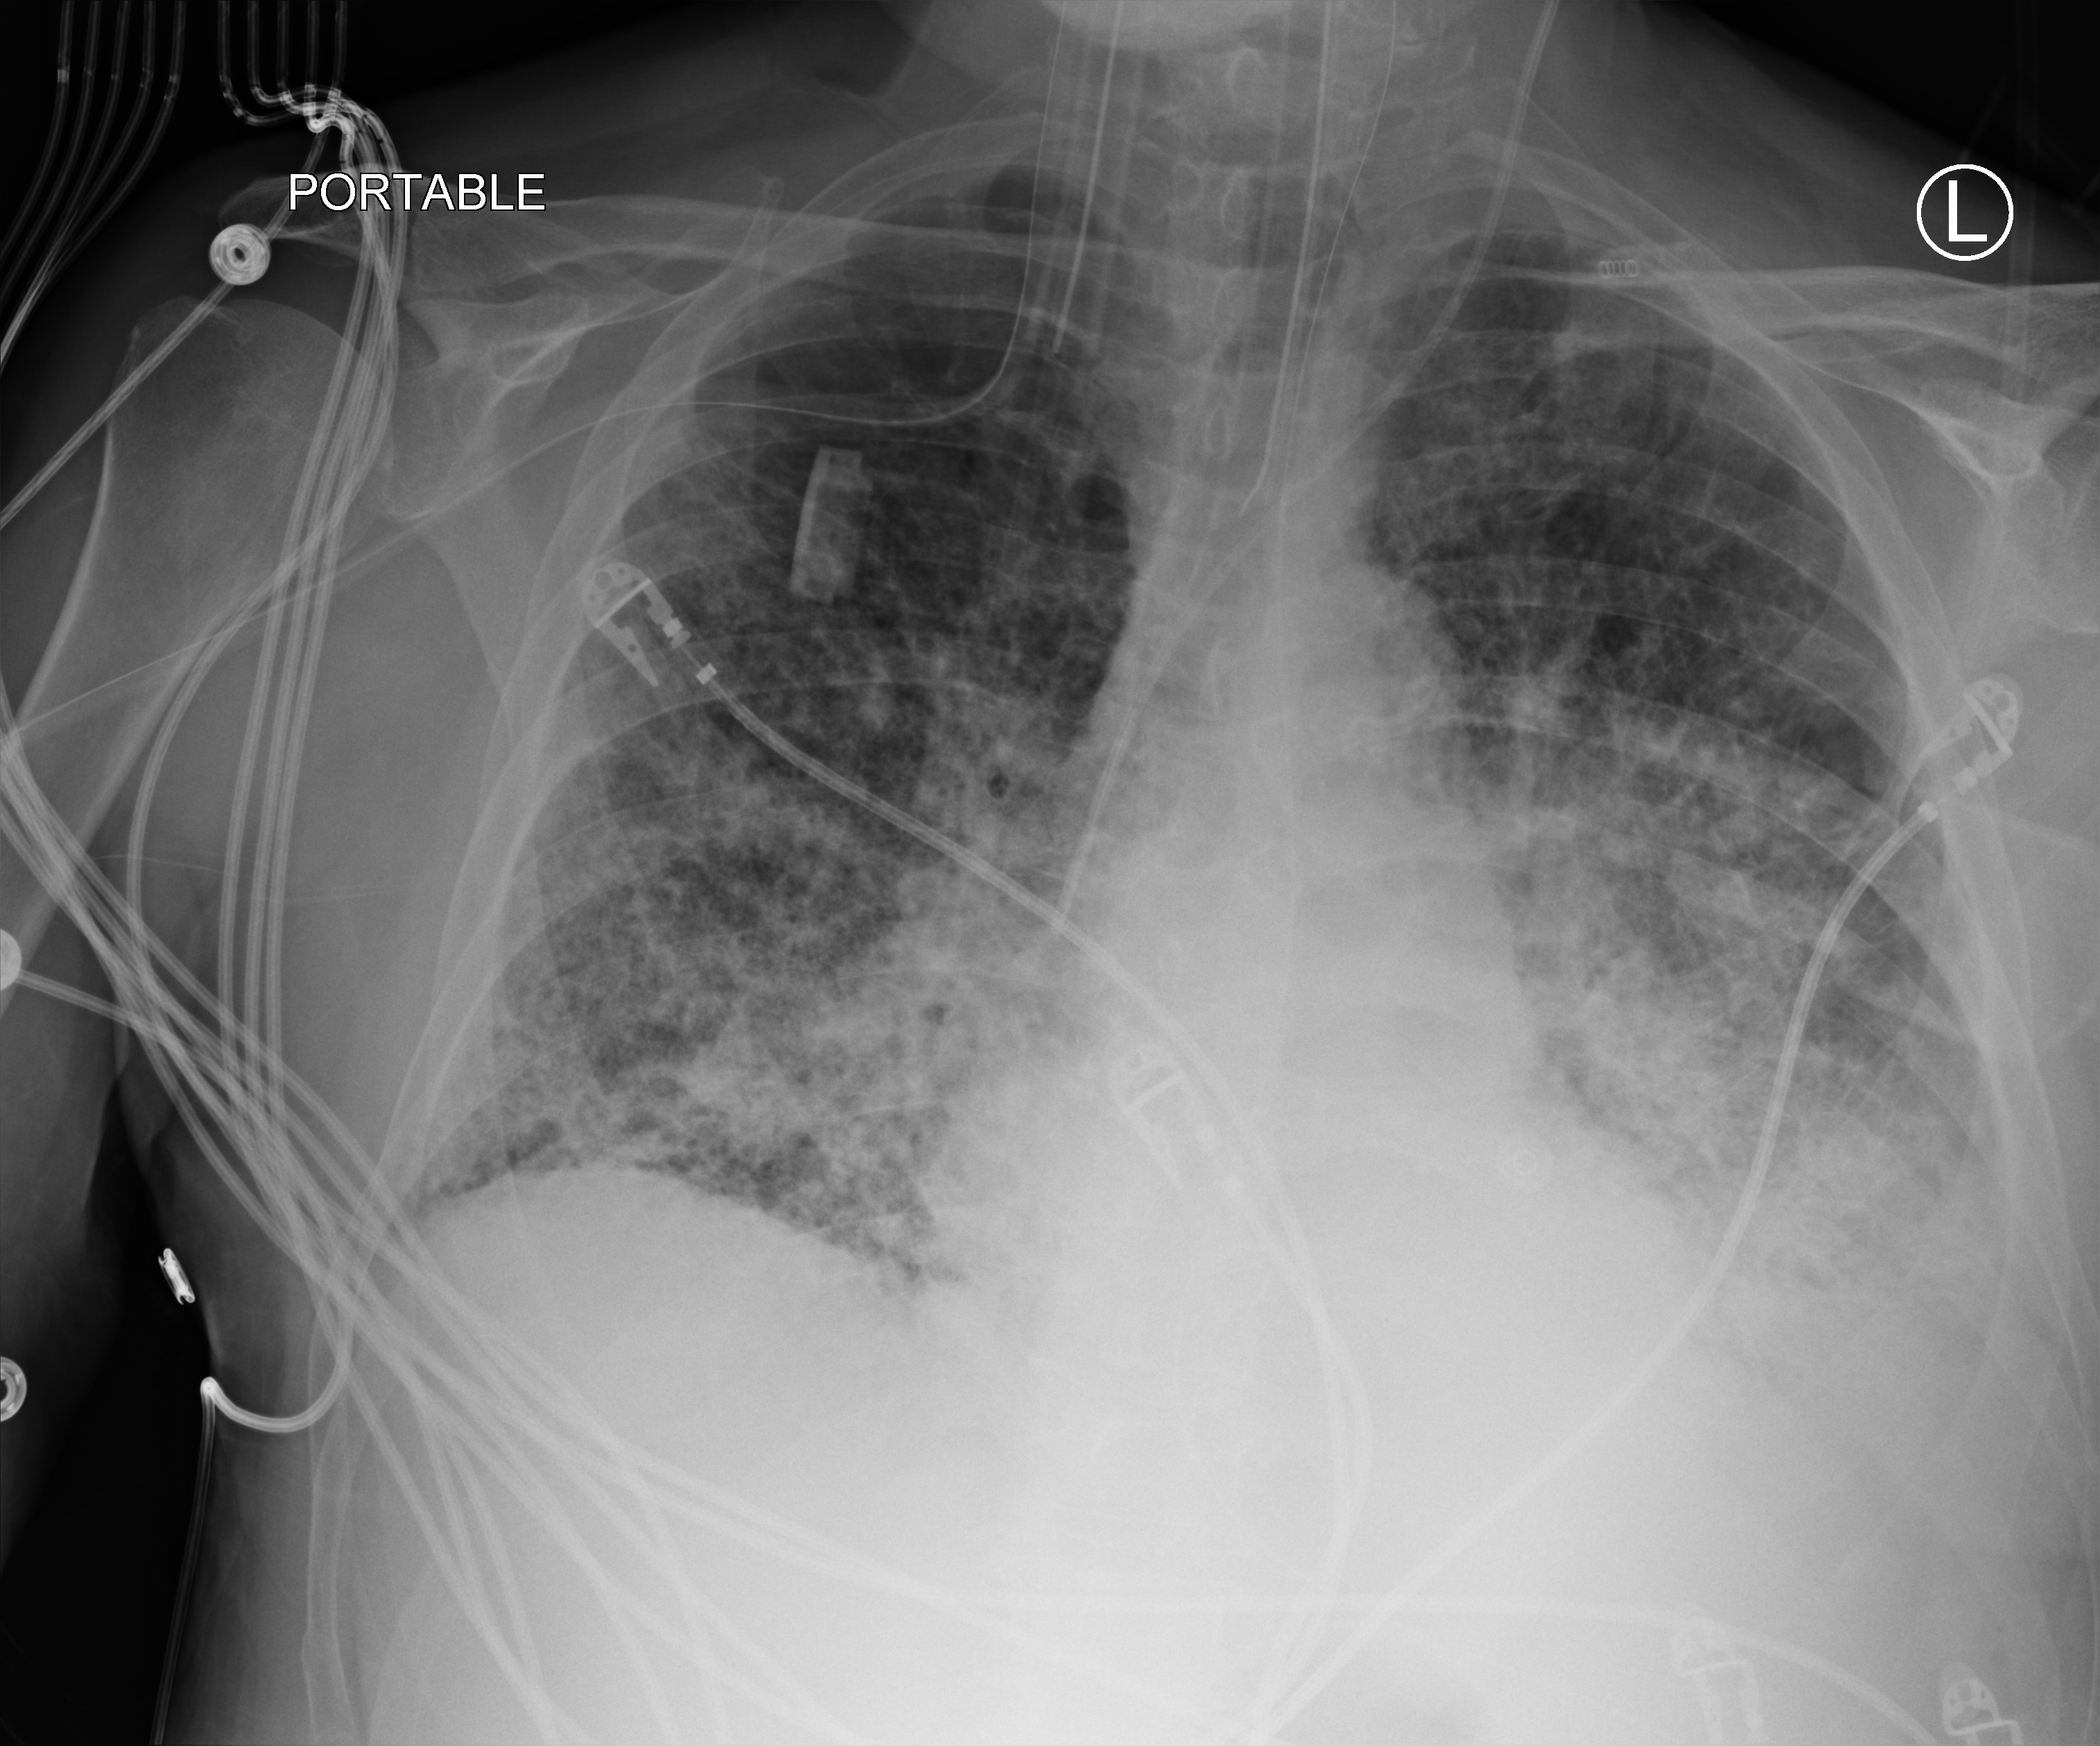
Bedside chest radiograph (computed radiography), anteroposterior (AP) projection. Male patient hospitalised with COVID-19, age 75–90 years.
Hospital-stay facts (about this admission, not read from this image; timing relative to this image not recorded):
- admitted to intensive care during this hospital stay: yes
- diabetes (admission record): no
- other chronic lung disease (admission record): yes